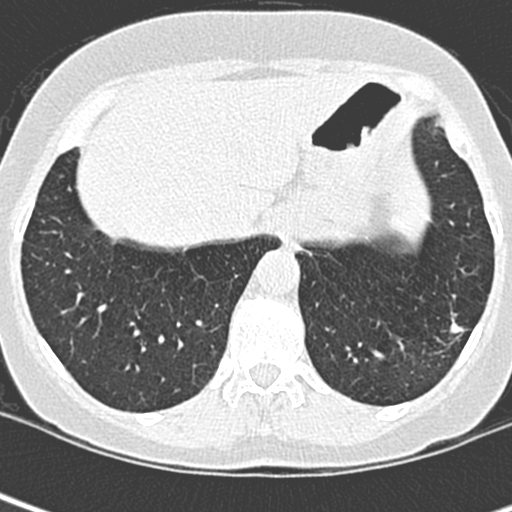
Low-dose screening chest CT, one axial slice. Slice 60 of 252 in the series (ordered by position). 120 kVp. Lung window (W 1500 / L -600 HU). 512 × 512 image matrix, field of view 271 × 271 mm.
Structures marked on this image (expert manual segmentation):
- lesion 1 (tumor, lower lobe of left lung): bounding box [x1, y1, x2, y2] px = [450, 319, 464, 337]